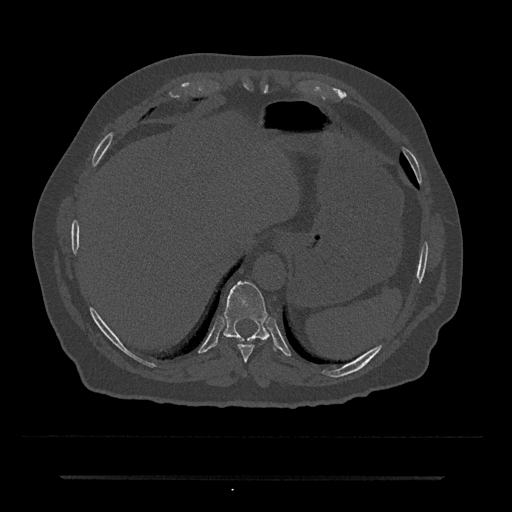
CT including the spine, one axial slice; 120 kVp; bone window (W 1800 / L 400 HU); 0.5 mm slice thickness; 512 × 512 image matrix, field of view 437 × 437 mm. Male patient, age 69 years. Case-level facts recorded for this patient, not image findings: primary cancer: prostate.
Annotated regions visible in this slice (semi-automatic segmentation, software-assisted and operator-edited):
- T10 vertebra: box from (x=223, y=281) to (x=269, y=342) px
- T9 vertebra: (x=238, y=344)–(x=255, y=362)